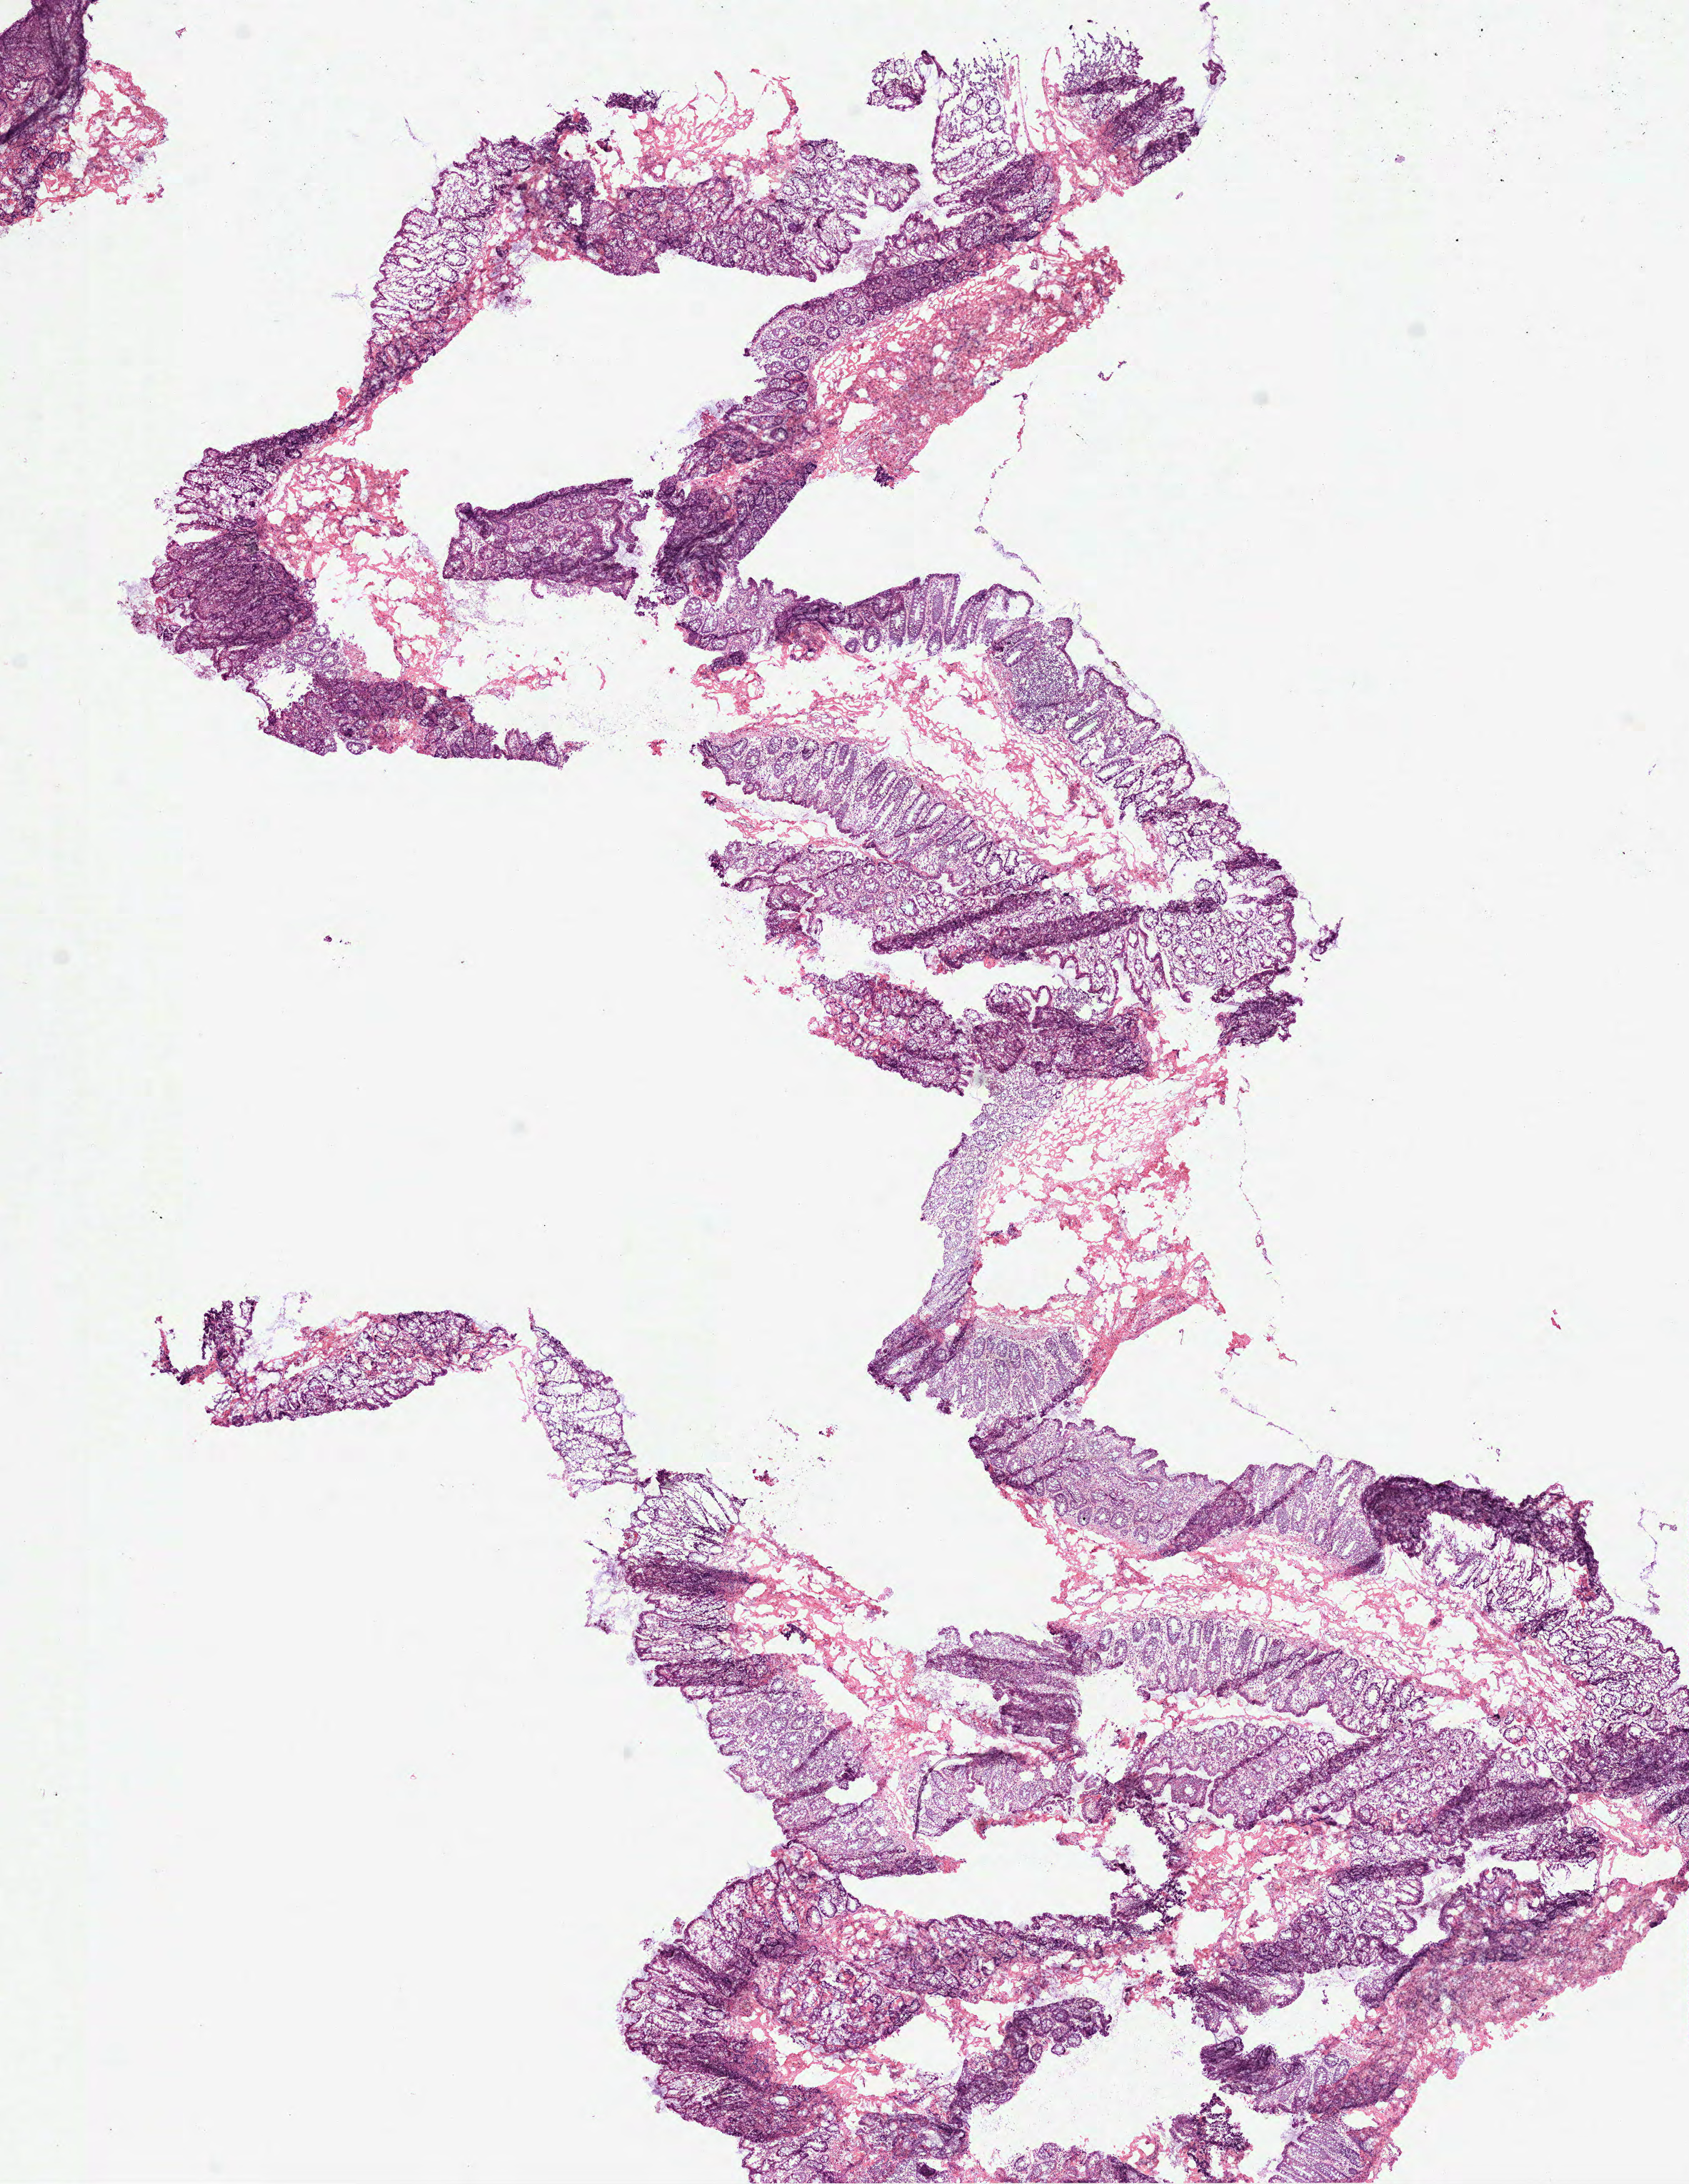
Whole-slide histology image, H&E-stained, shown as a low-resolution overview of the whole scanned area (about 9.5 x 12.3 mm, acquisition: 40x scan); frozen section from the top of the tissue portion; colon, solid tissue normal (non-tumour tissue) sample. Female, age 76 years at initial diagnosis.
This section: solid tissue normal (non-tumour) sample from the same patient. Patient diagnosis: Adenocarcinoma, NOS (cecum).